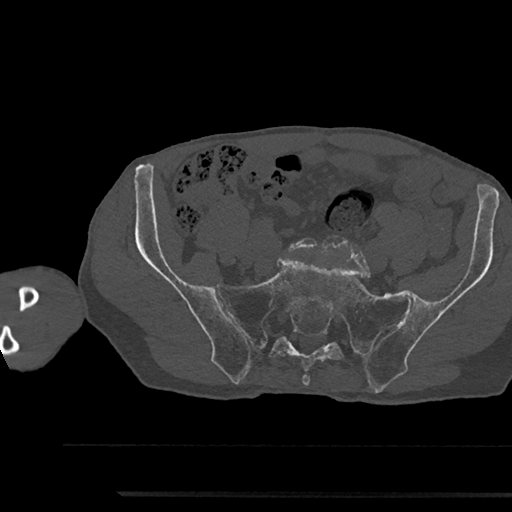
CT including the spine, one axial slice; slice 279 of 797 in the series (ordered by position); bone window (W 1800 / L 400 HU); 512 × 512 image matrix, field of view 367 × 367 mm. Male patient, age 79 years. From the clinical record (not read from this slice): primary cancer: prostate.
Structures marked on this image (semi-automatic segmentation, software-assisted and operator-edited):
- L5 vertebra: bounding box <289,238,317,251> (left, top, right, bottom; pixels)